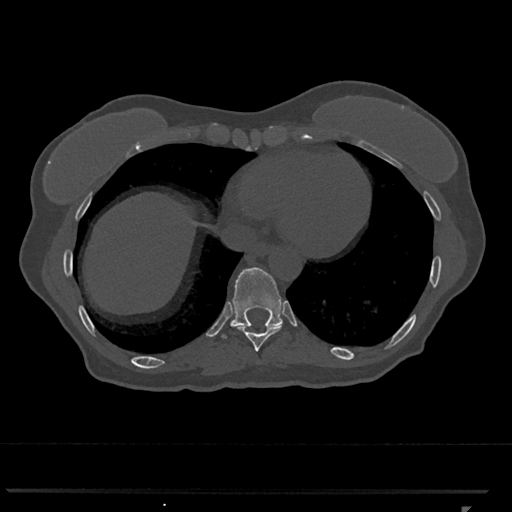
CT including the spine, one axial slice. Position 594 of 793 along the scan axis. 120 kVp. Bone window (W 1800 / L 400 HU). 512 × 512 image matrix, field of view 380 × 380 mm. Female patient, age 62 years. From the clinical record (not read from this slice): primary cancer: renal.
Structures marked on this image (semi-automatic segmentation, software-assisted and operator-edited):
- T10 vertebra: bounding box <222,267,283,338> (left, top, right, bottom; pixels)
- T9 vertebra: <234,323,283,351>